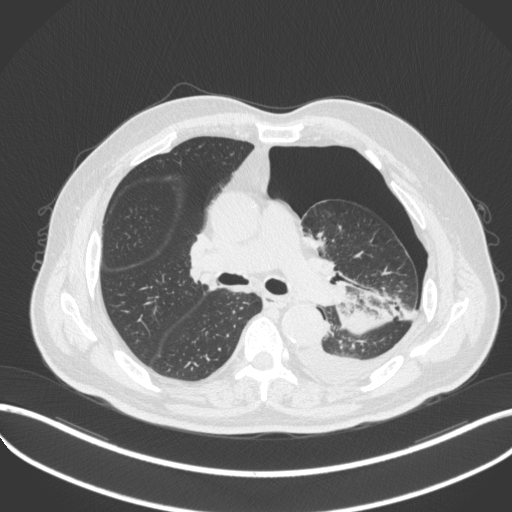
Chest CT, one axial slice; slice 314 of 466 in the series (ordered by position); reconstruction kernel B31f; lung window (W 1500 / L -600 HU); 1 mm slice thickness; 512 × 512 image matrix, field of view 400 × 400 mm. Male patient, age 76 years. Case-level facts recorded for this patient, not image findings: clinical TNM (as recorded): T3 N0 M1b.
Outlined on this slice (bounding box drawn by a radiologist):
- lung tumour (recorded histology: adenocarcinoma): bounding box (x1, y1, x2, y2) in pixels: (323, 275, 397, 339)